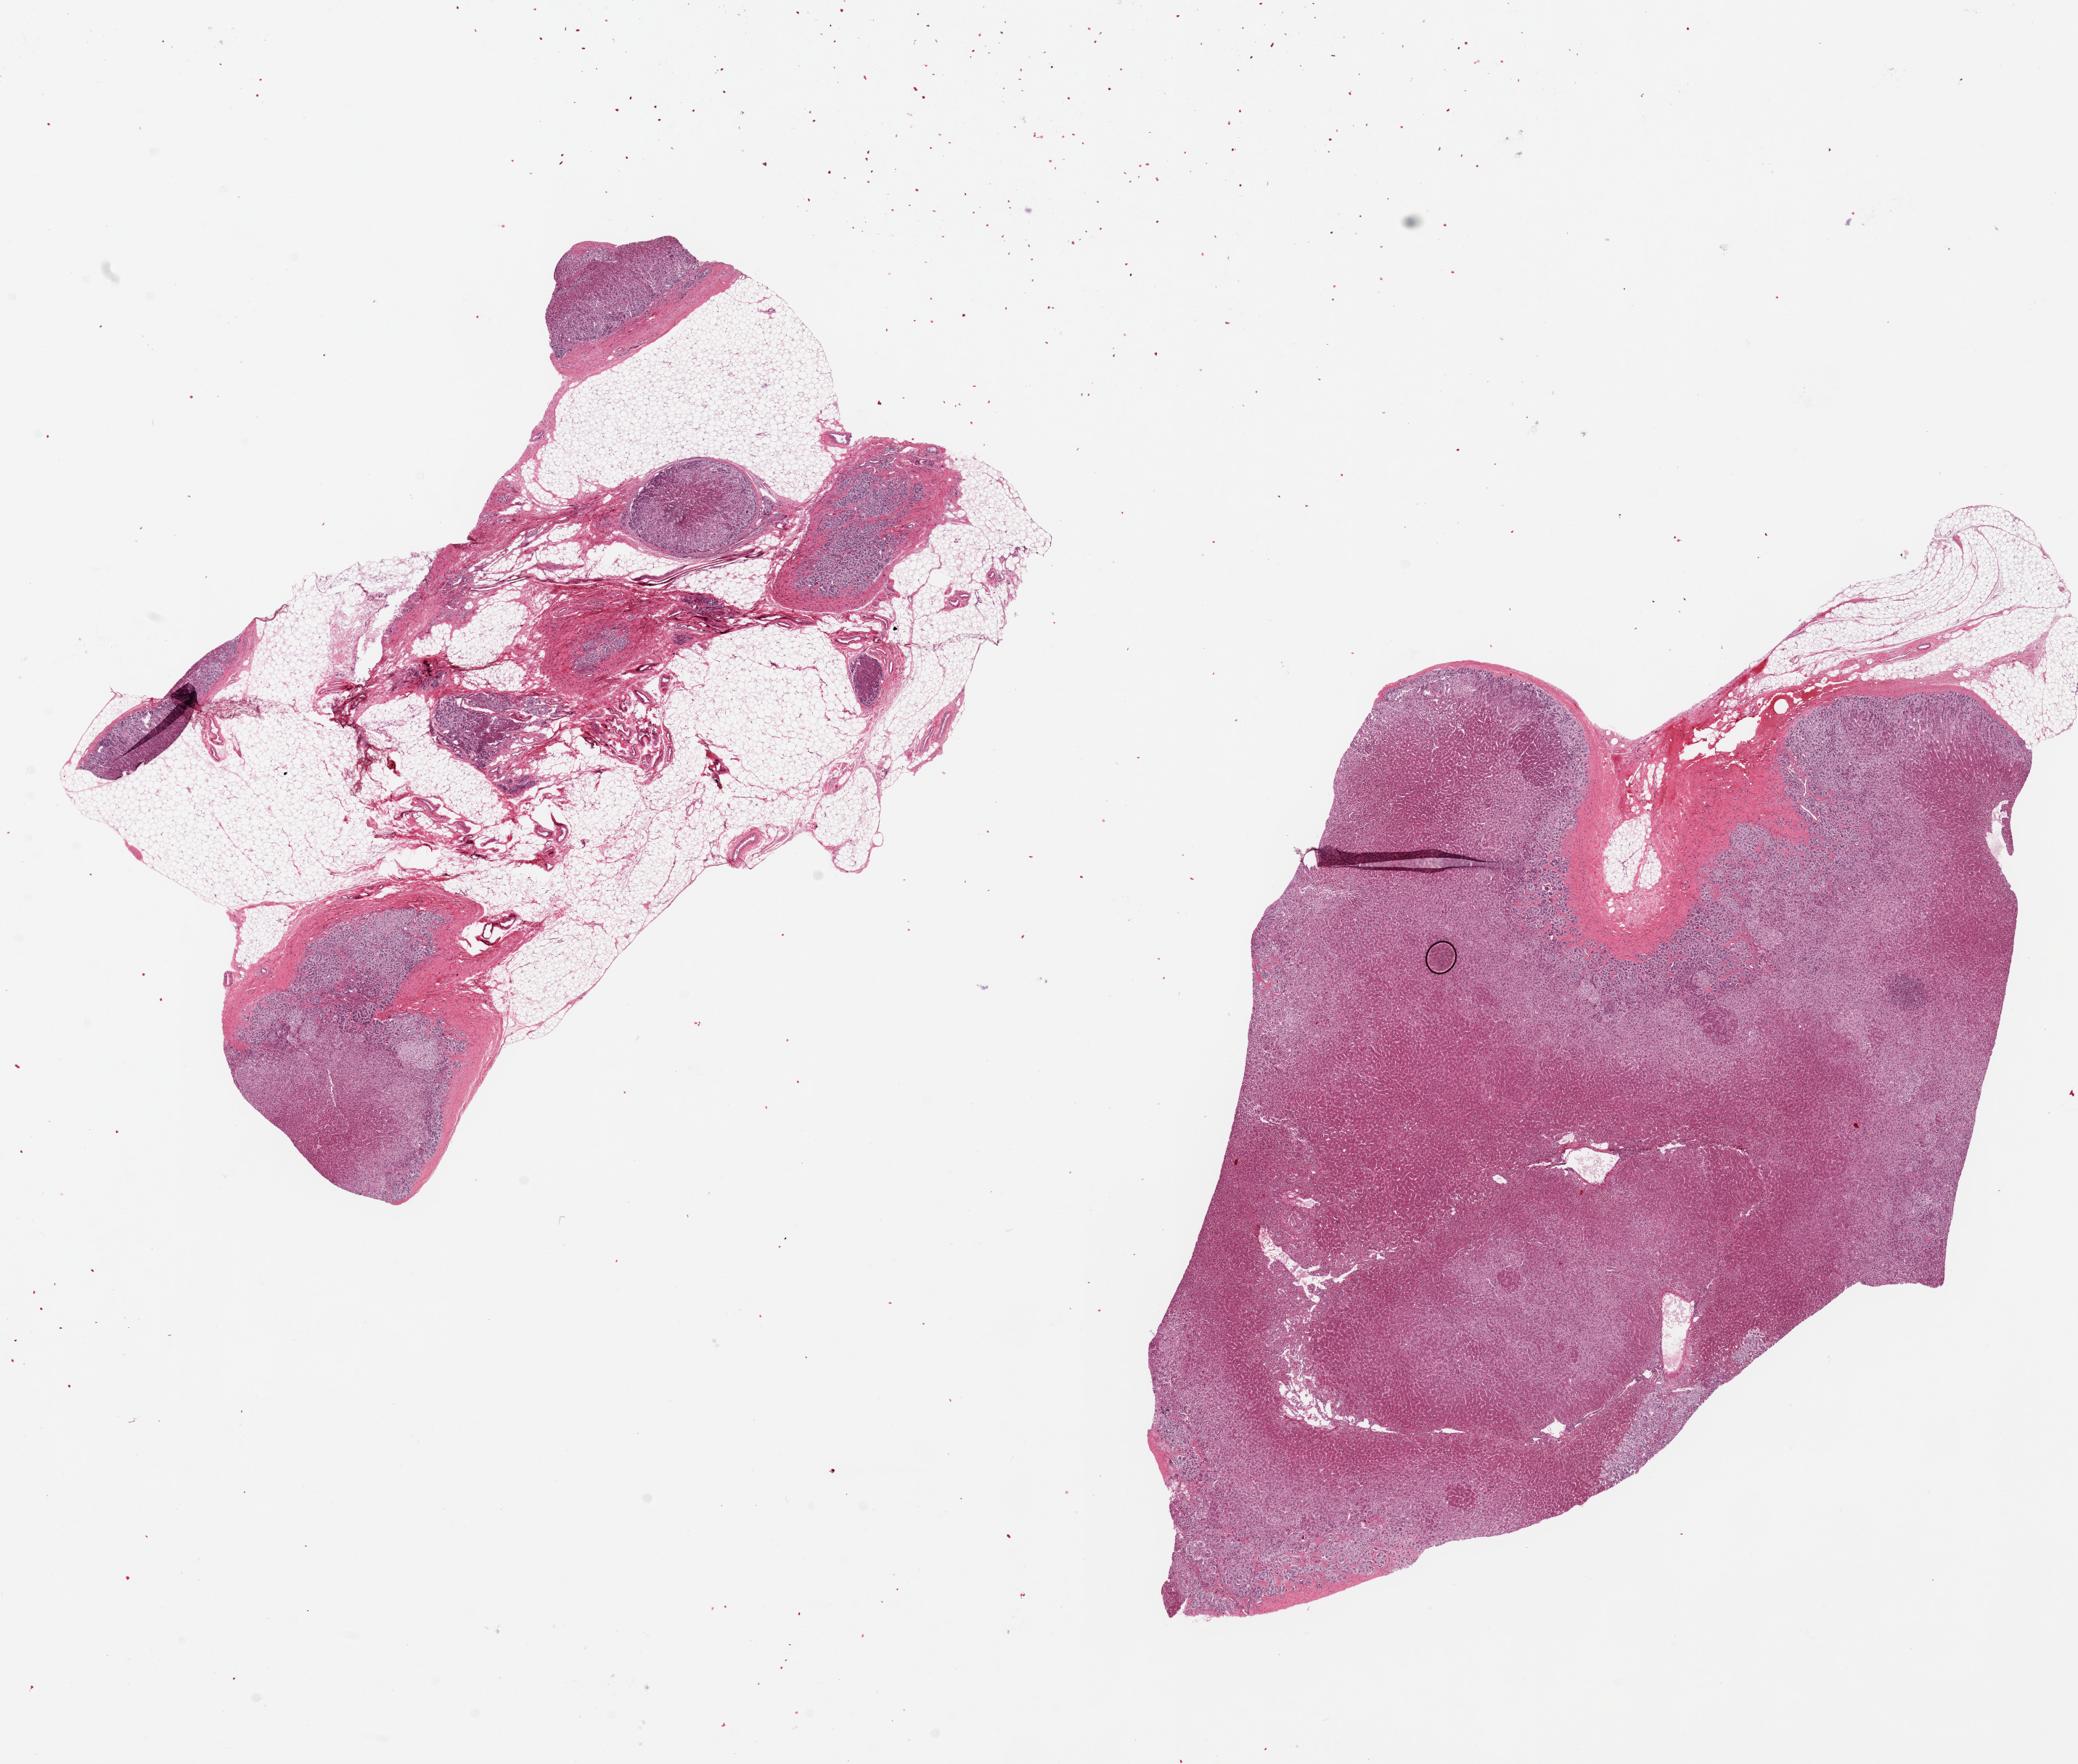
Whole-slide image, H&E stain, low-resolution overview of the scanned area, about 22.6 x 19.2 mm; PAXgene-fixed paraffin-embedded (PFPE) section; target tissue: adrenal gland; tissue donor sample. Donor sex: female.
Pathologist's review note for this sample: 2 pieces, 11x7 & 12x11mm; one is 60-70% interstitial and adherent fat, other is ~20% fat; Cortical areas well preserved.